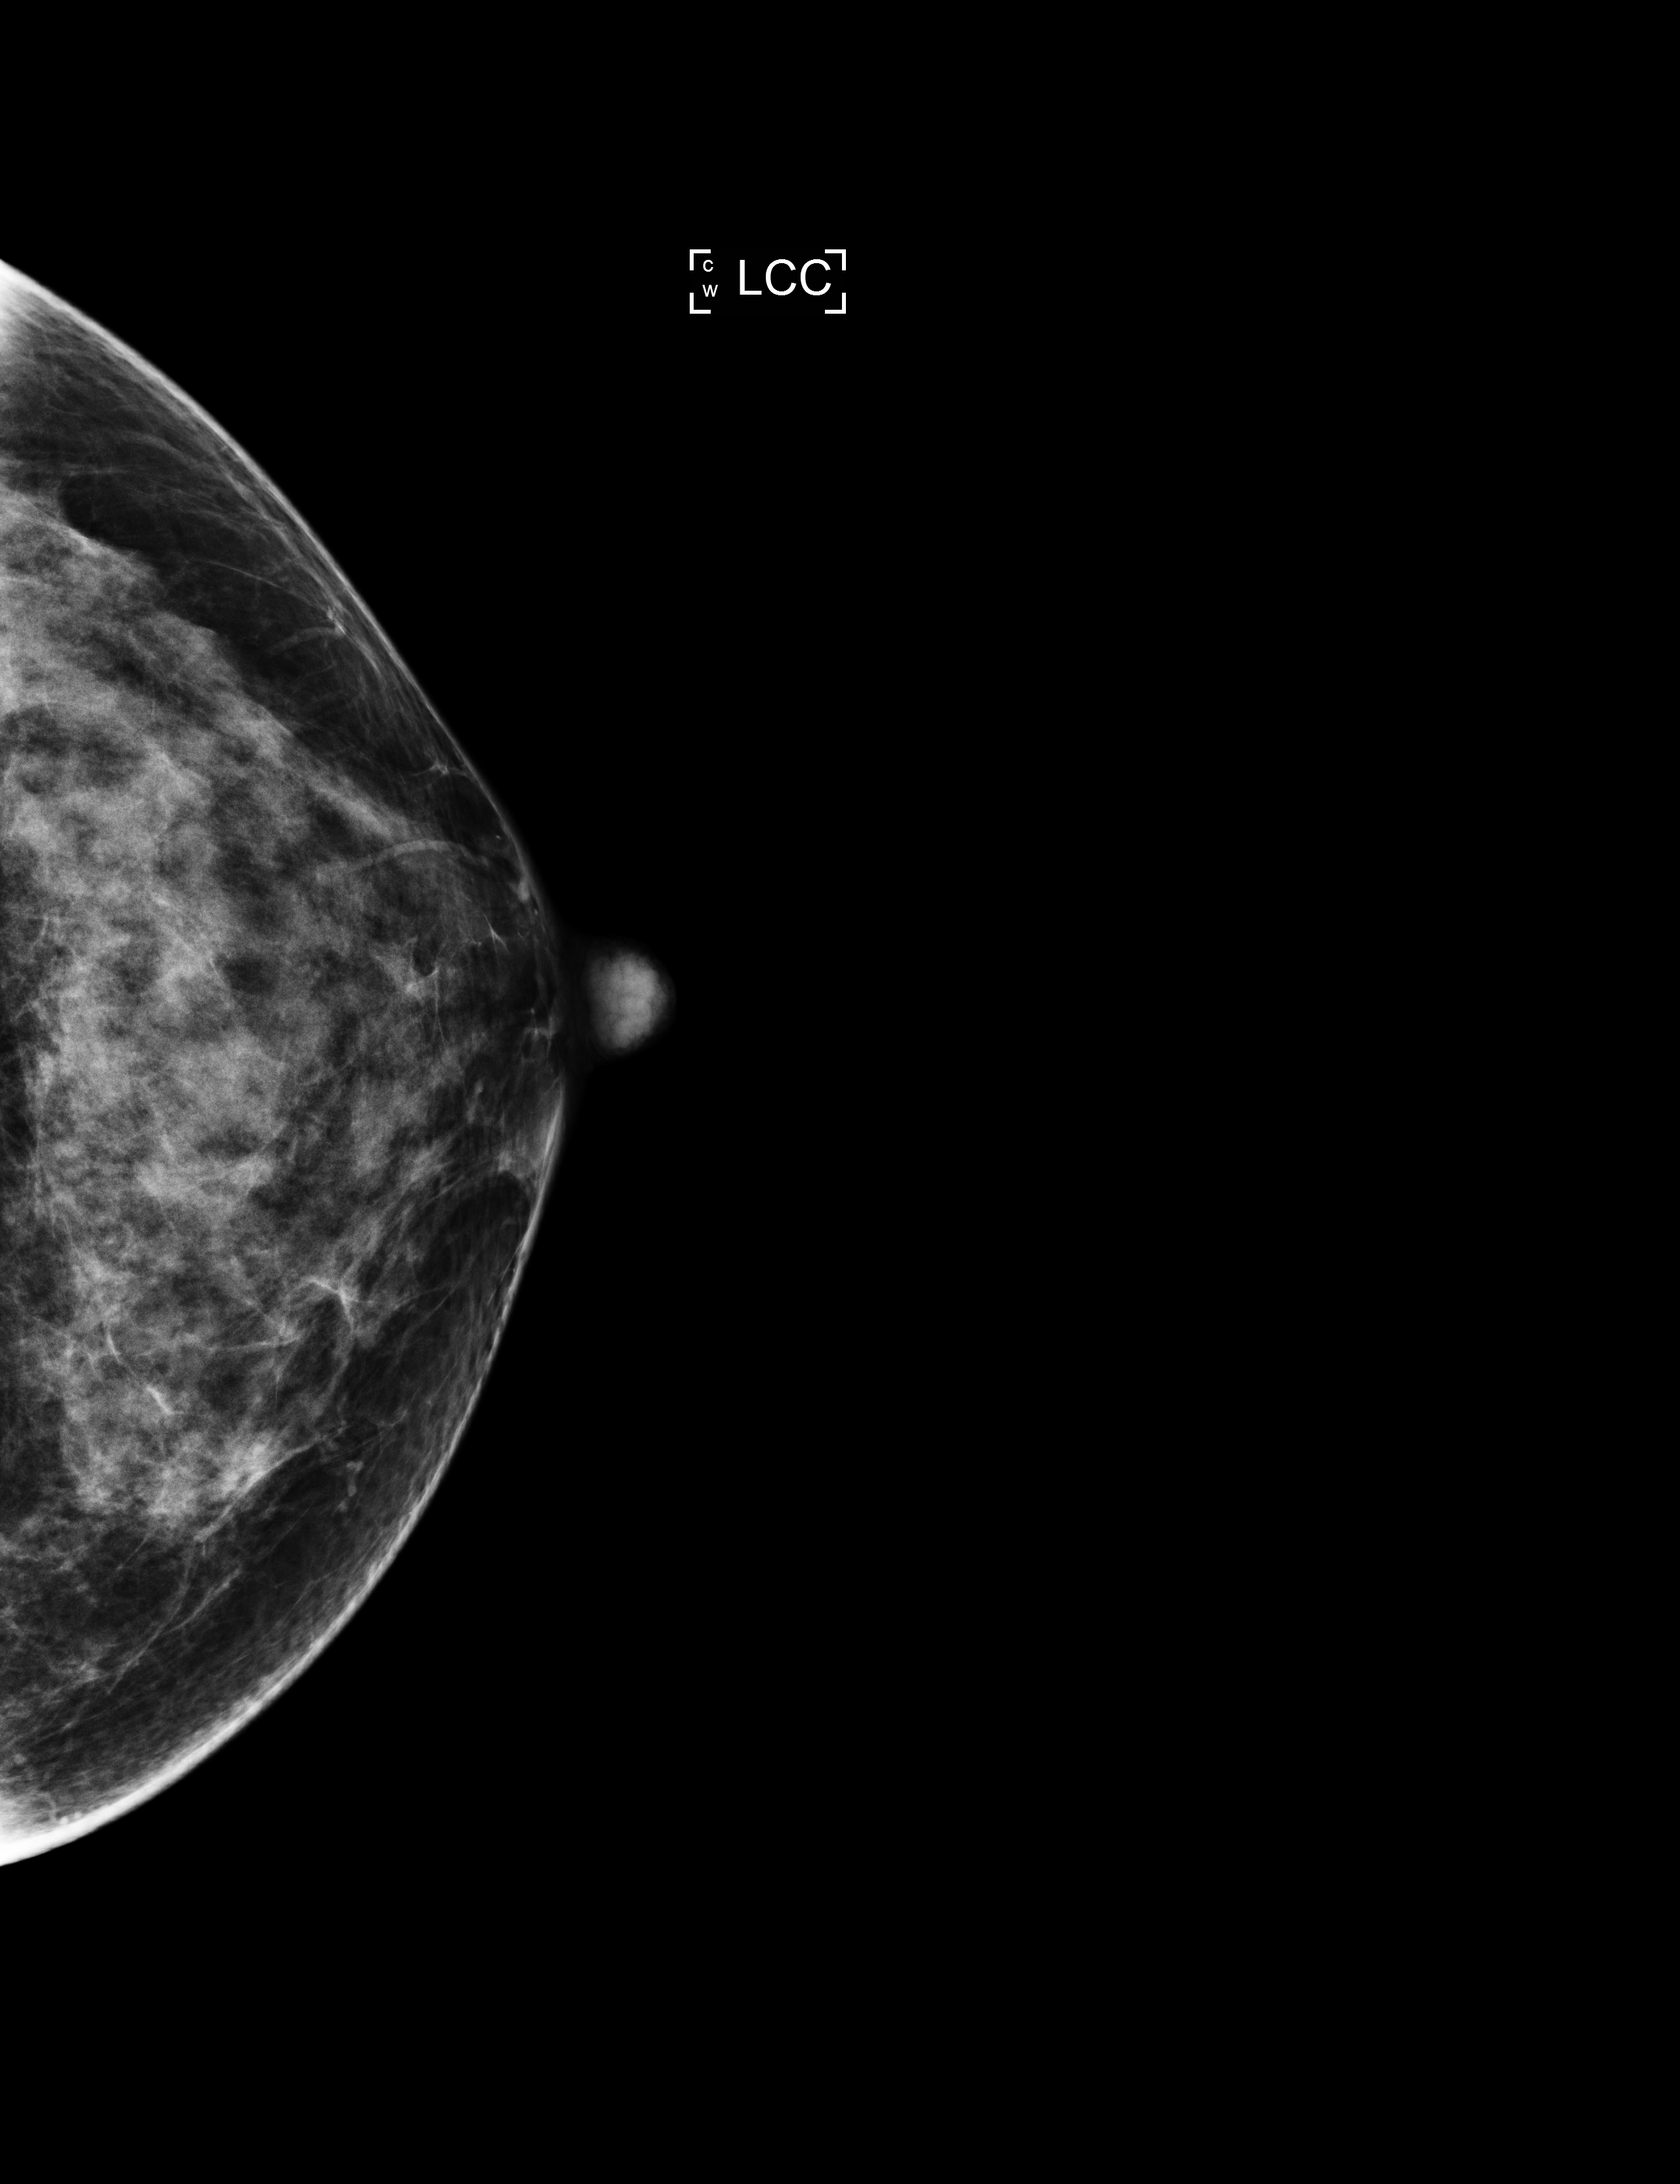
Full-field digital mammogram (FFDM); left breast; CC view; annual screening mammography examination; compressed breast thickness 61 mm. Female patient, age 41 years.
Final BI-RADS assessment for this screening round (tomosynthesis exam, both breasts): category 1.